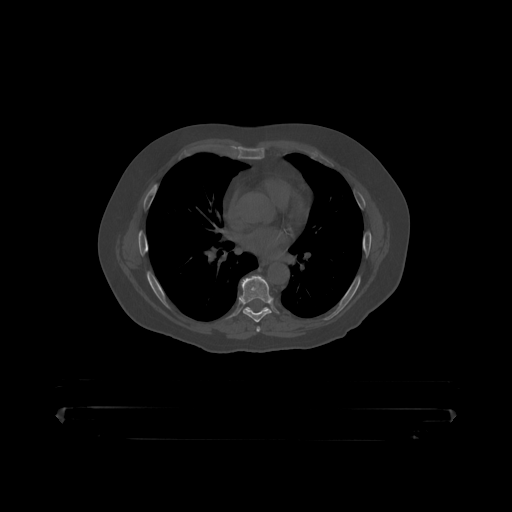
CT including the spine, one axial slice; slice 276 of 390 in the series (ordered by position); reconstruction kernel STANDARD; 120 kVp; bone window (W 1800 / L 400 HU); 512 × 512 image matrix, field of view 650 × 650 mm. Male patient, age 60 years. From the clinical record (not read from this slice): primary cancer: prostate.
Outlined on this slice (semi-automatic segmentation, software-assisted and operator-edited):
- T7 vertebra: bounding box <241,276,273,319> (left, top, right, bottom; pixels)
- T8 vertebra: <246,307,269,310>